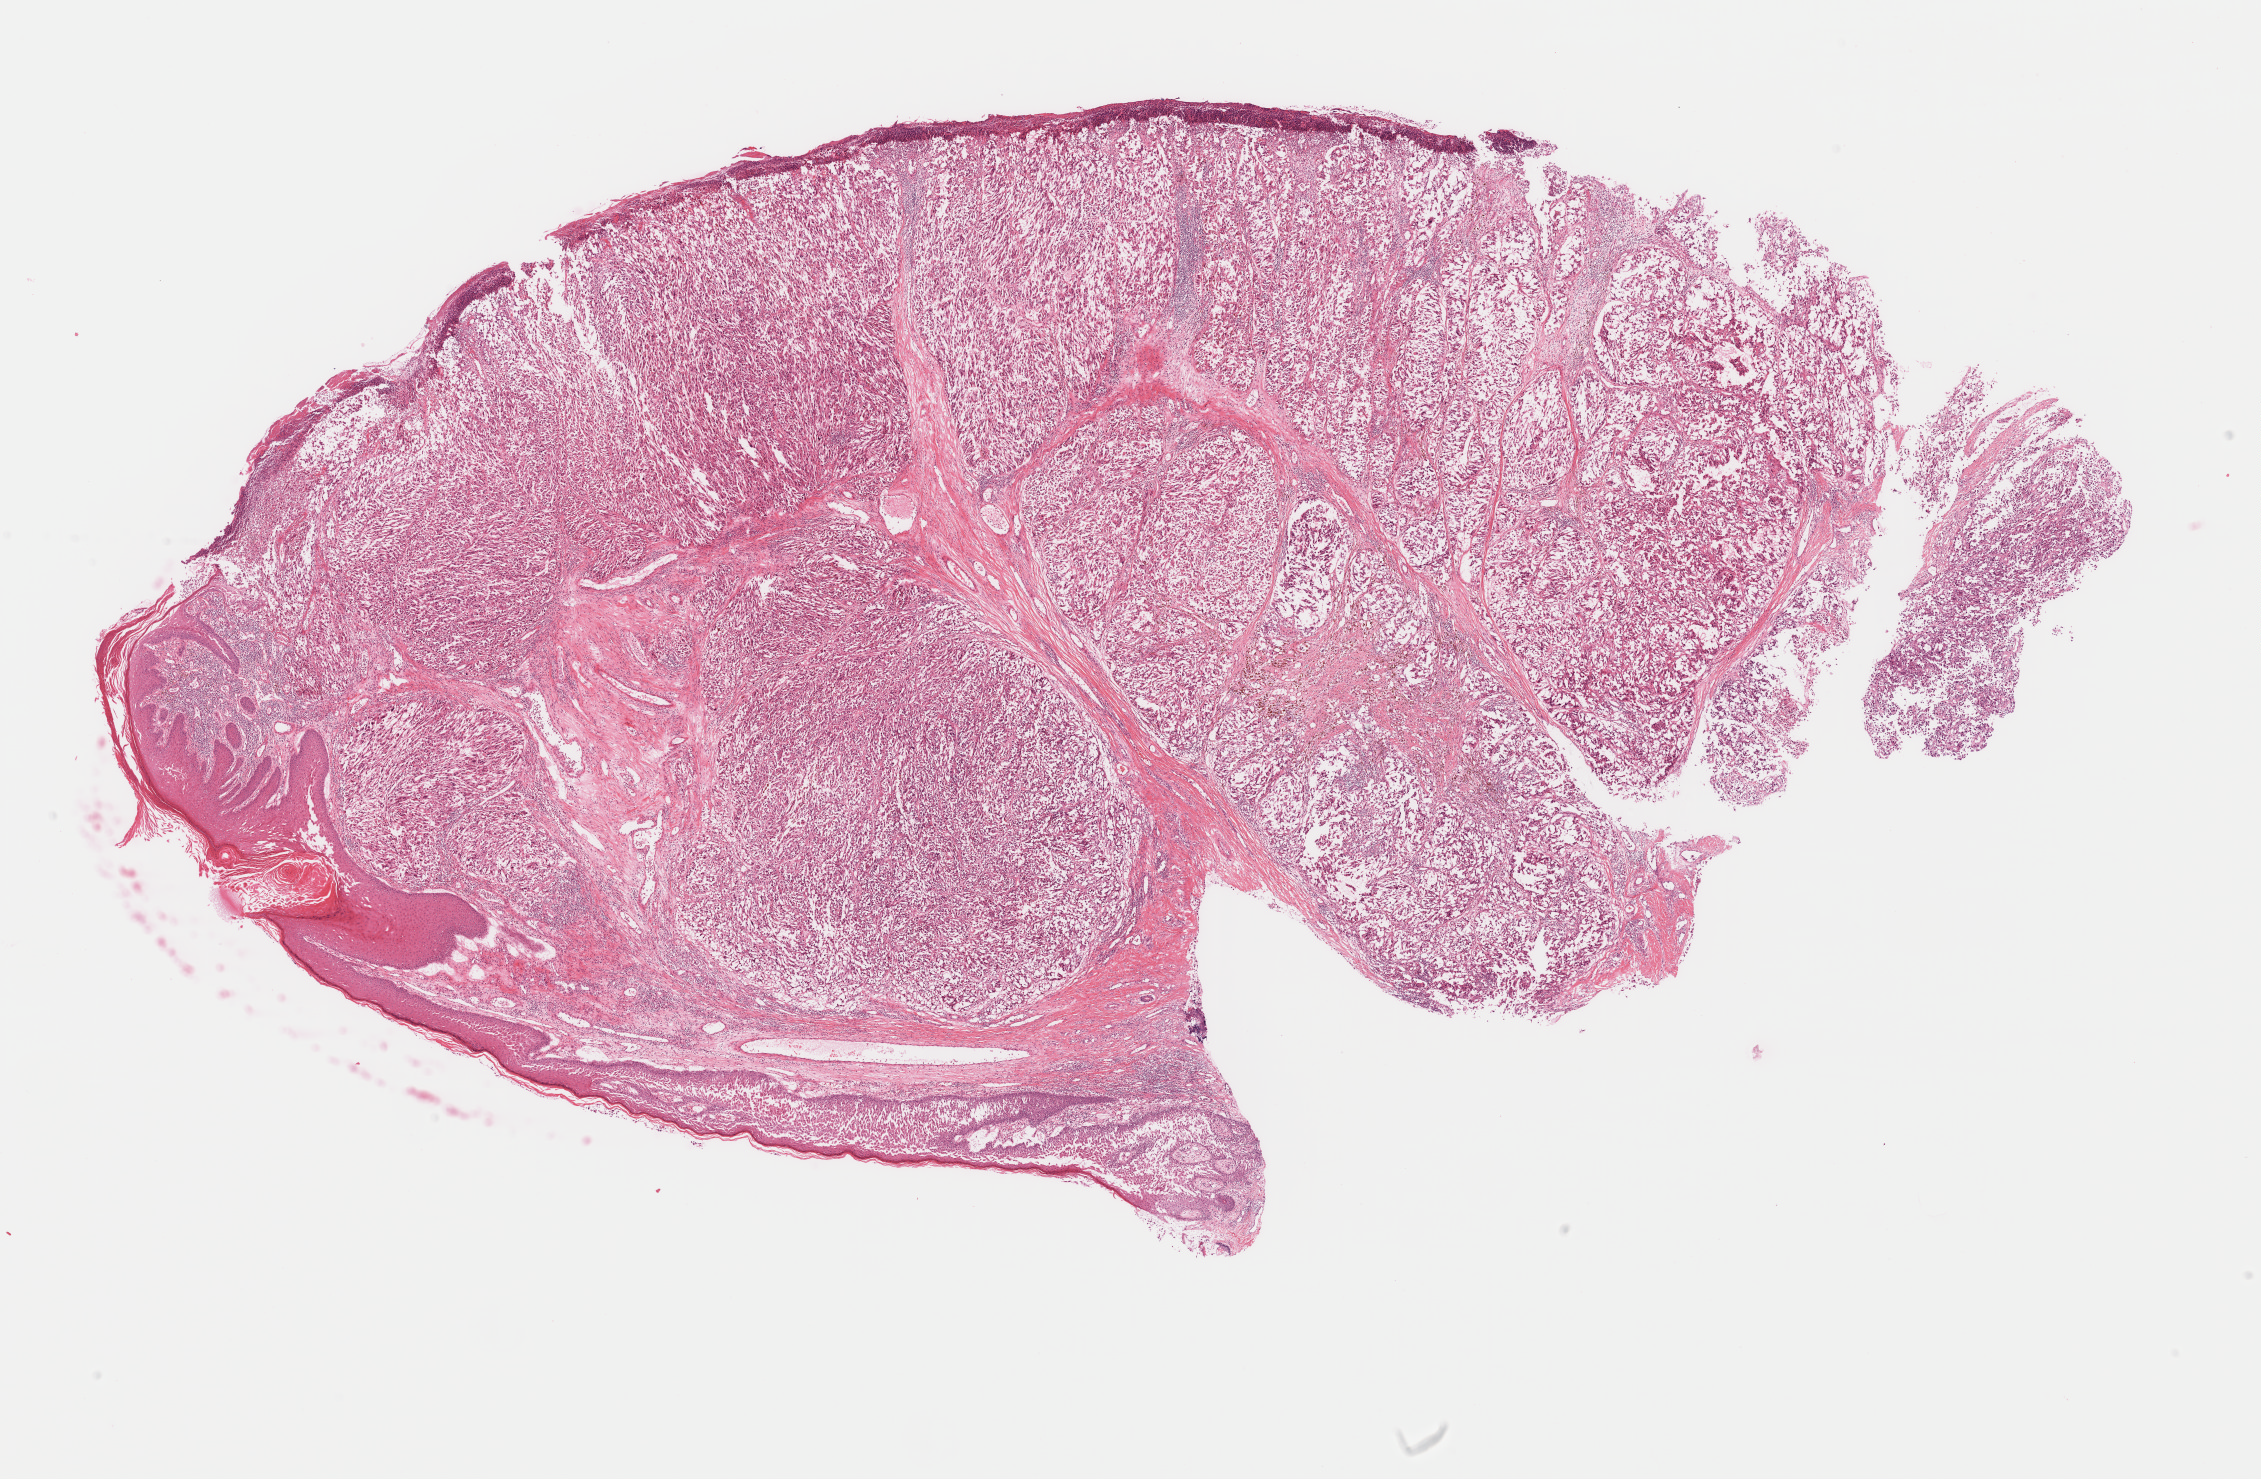
Digitized Hematoxylin and eosin (H&E) stained tissue section (whole slide), whole scanned area (about 17.9 x 11.7 mm) shown as a low-resolution overview. Formalin-fixed paraffin-embedded (FFPE) diagnostic section. Sample: primary tumour, skin. Male, age 34 years at initial diagnosis.
Diagnosis: Nodular melanoma.